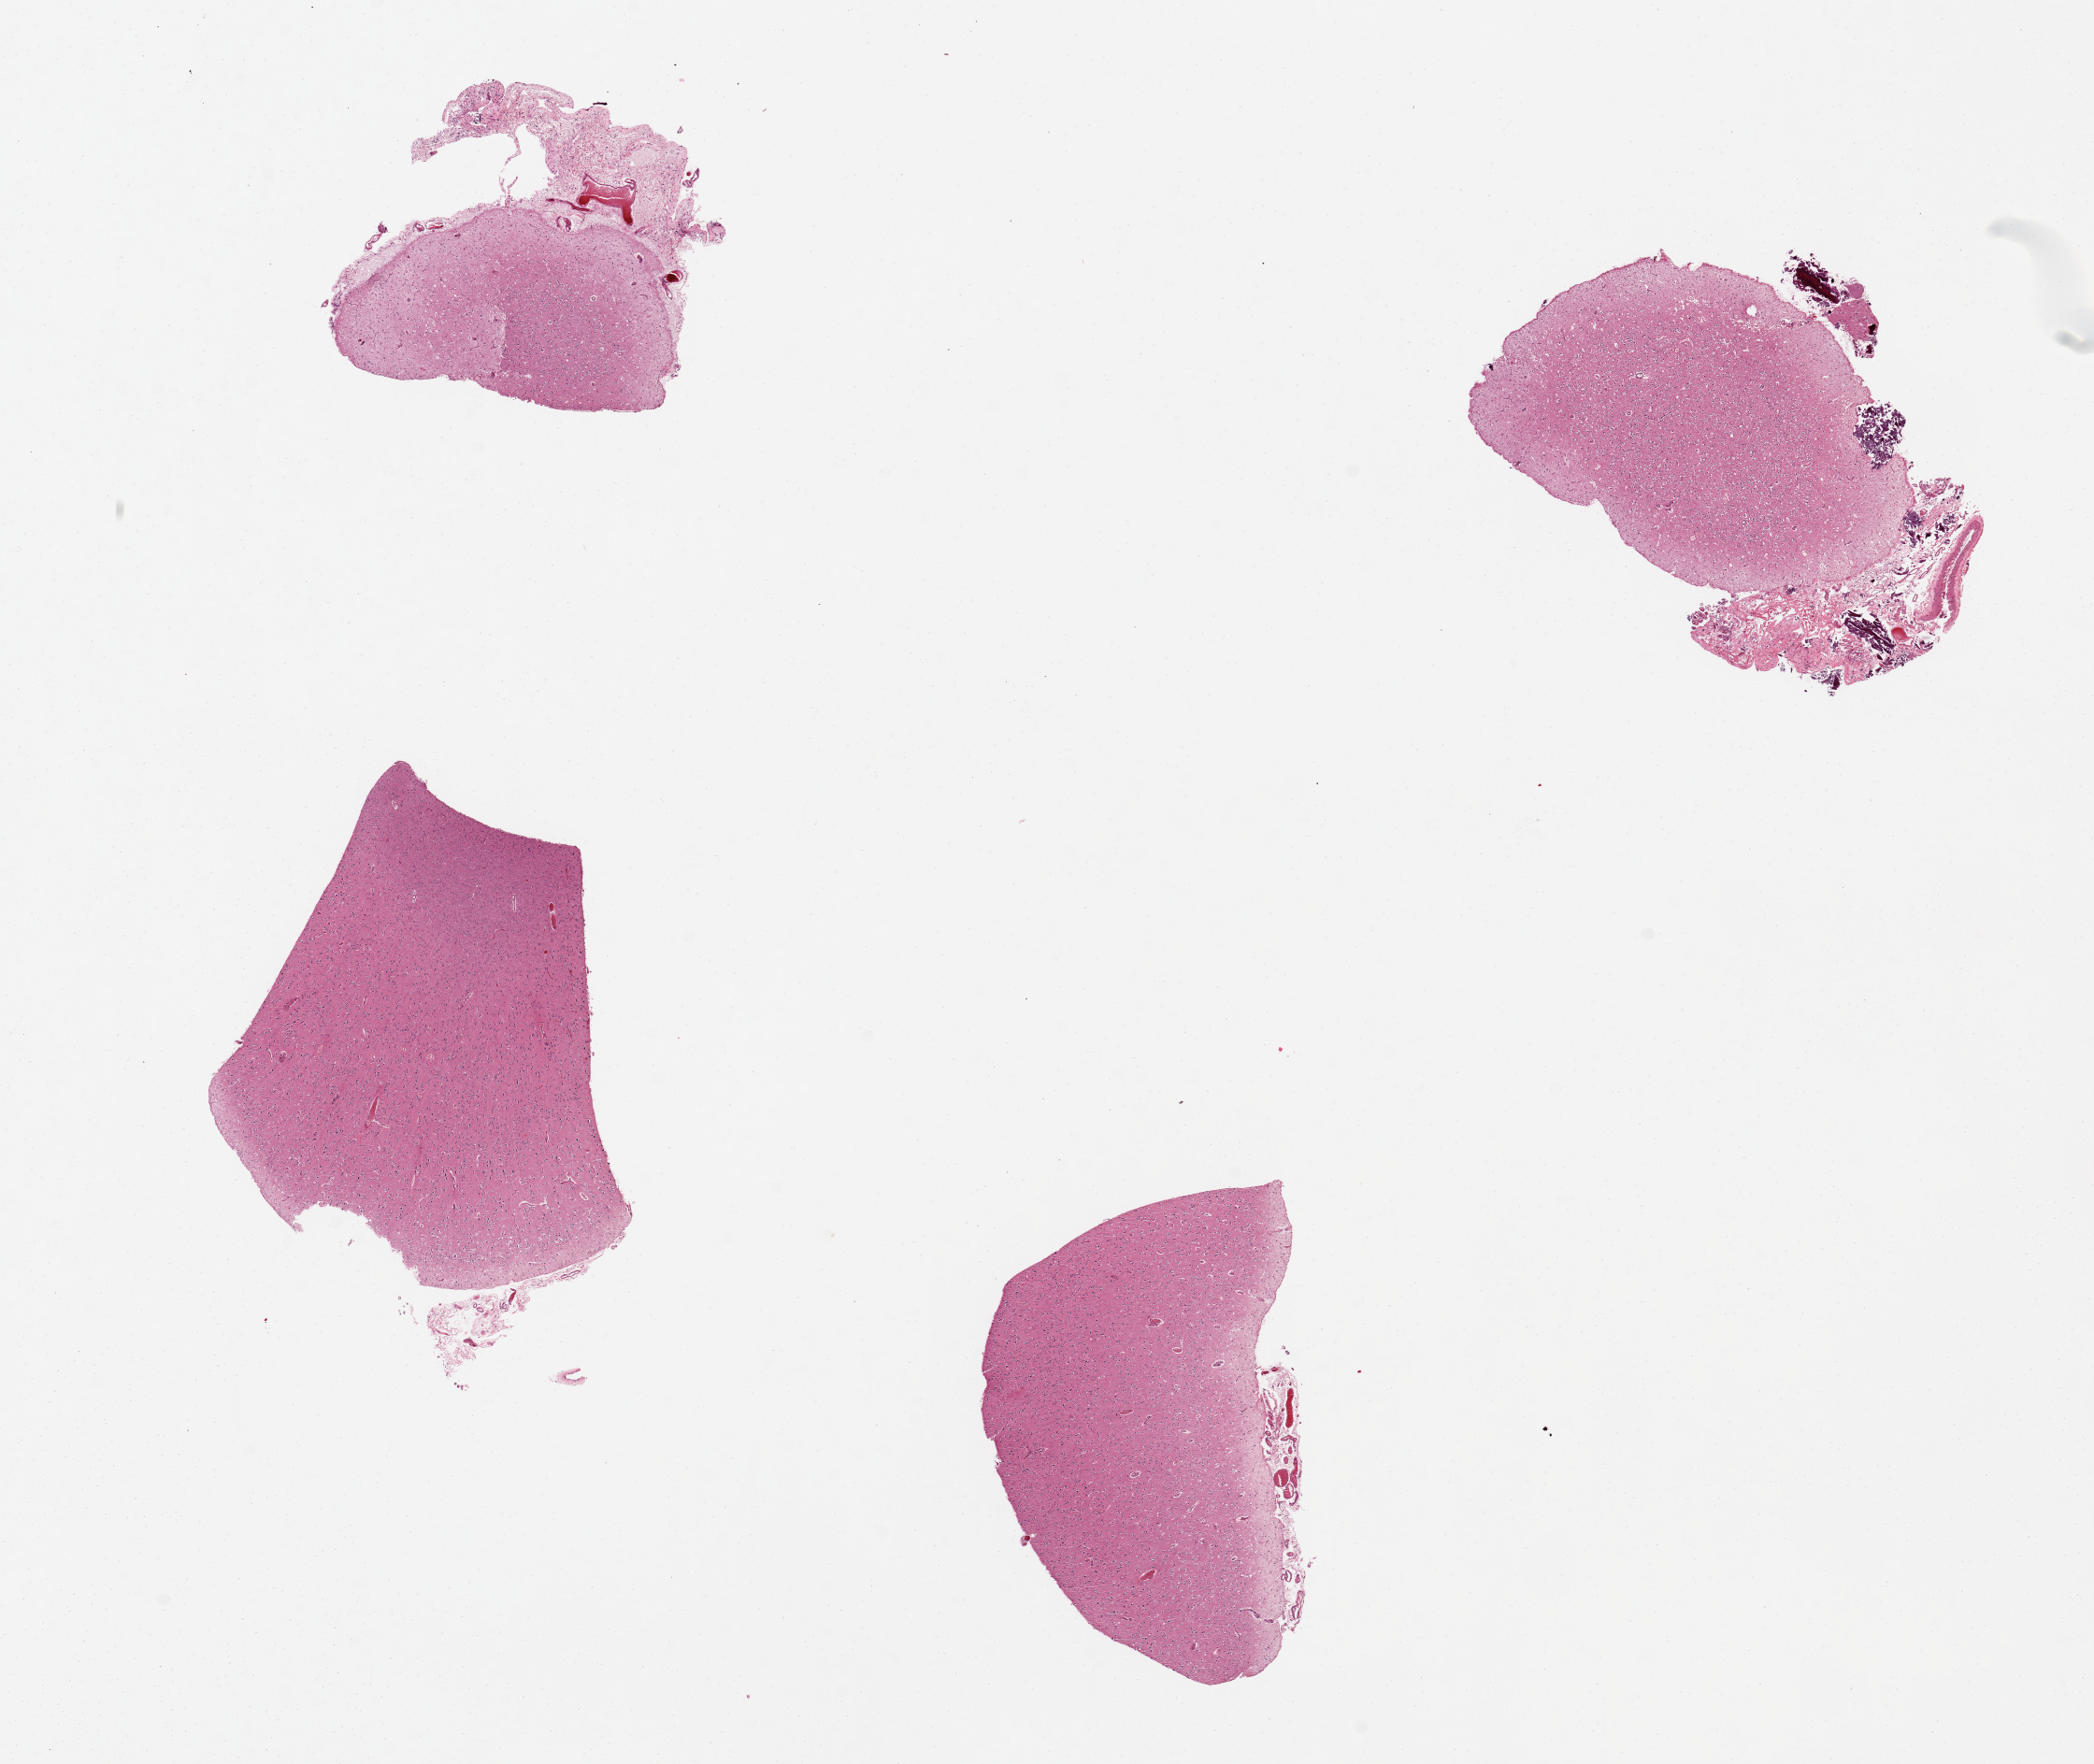
Haematoxylin and eosin whole-slide image, low-resolution overview of the scanned area, about 17.7 x 14.9 mm (acquisition: 20x scan); PAXgene-fixed, paraffin-embedded tissue; section of cerebral cortex (target tissue); tissue donor sample. Male donor.
Pathologist's review note for this sample: 4 pieces; 2 pieces have adherent meninges up to 2x1 mm.